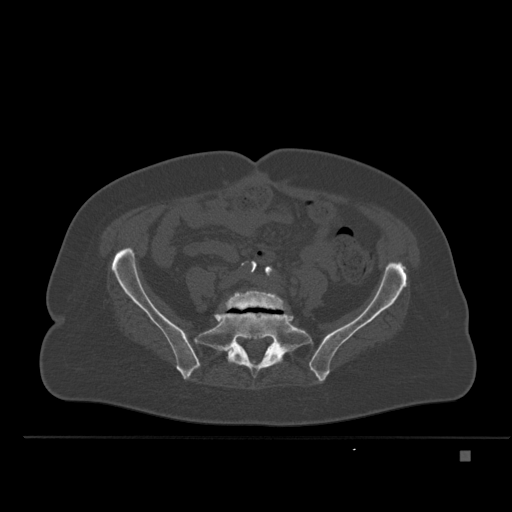
CT including the spine, one axial slice; slice 150 of 477 in the series (ordered by position); bone window (W 1800 / L 400 HU); 1.5 mm slice thickness; 512 × 512 image matrix. Female patient, age 74 years. From the clinical record (not read from this slice): primary cancer: colon.
Outlined on this slice (semi-automatic segmentation, software-assisted and operator-edited):
- L5 vertebra: bounding box (x1, y1, x2, y2) in pixels: (225, 290, 285, 310)